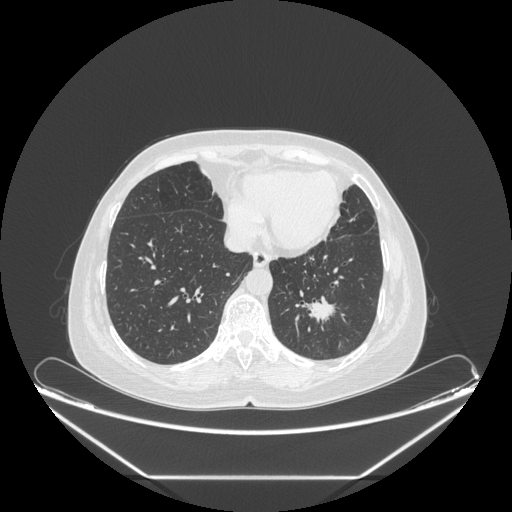
Chest CT, one axial slice. Position 77 of 241 along the scan axis. Lung window (W 1500 / L -600 HU). 1.25 mm slice thickness. 512 × 512 image matrix, field of view 451 × 451 mm. Patient: female, 63 years. From the clinical record (not read from this slice): clinical TNM (as recorded): T1c N0 M0.
Outlined on this slice (rectangle marked by the reading radiologist):
- lung tumour (recorded histology: adenocarcinoma): bounding box <295,288,340,330> (left, top, right, bottom; pixels)